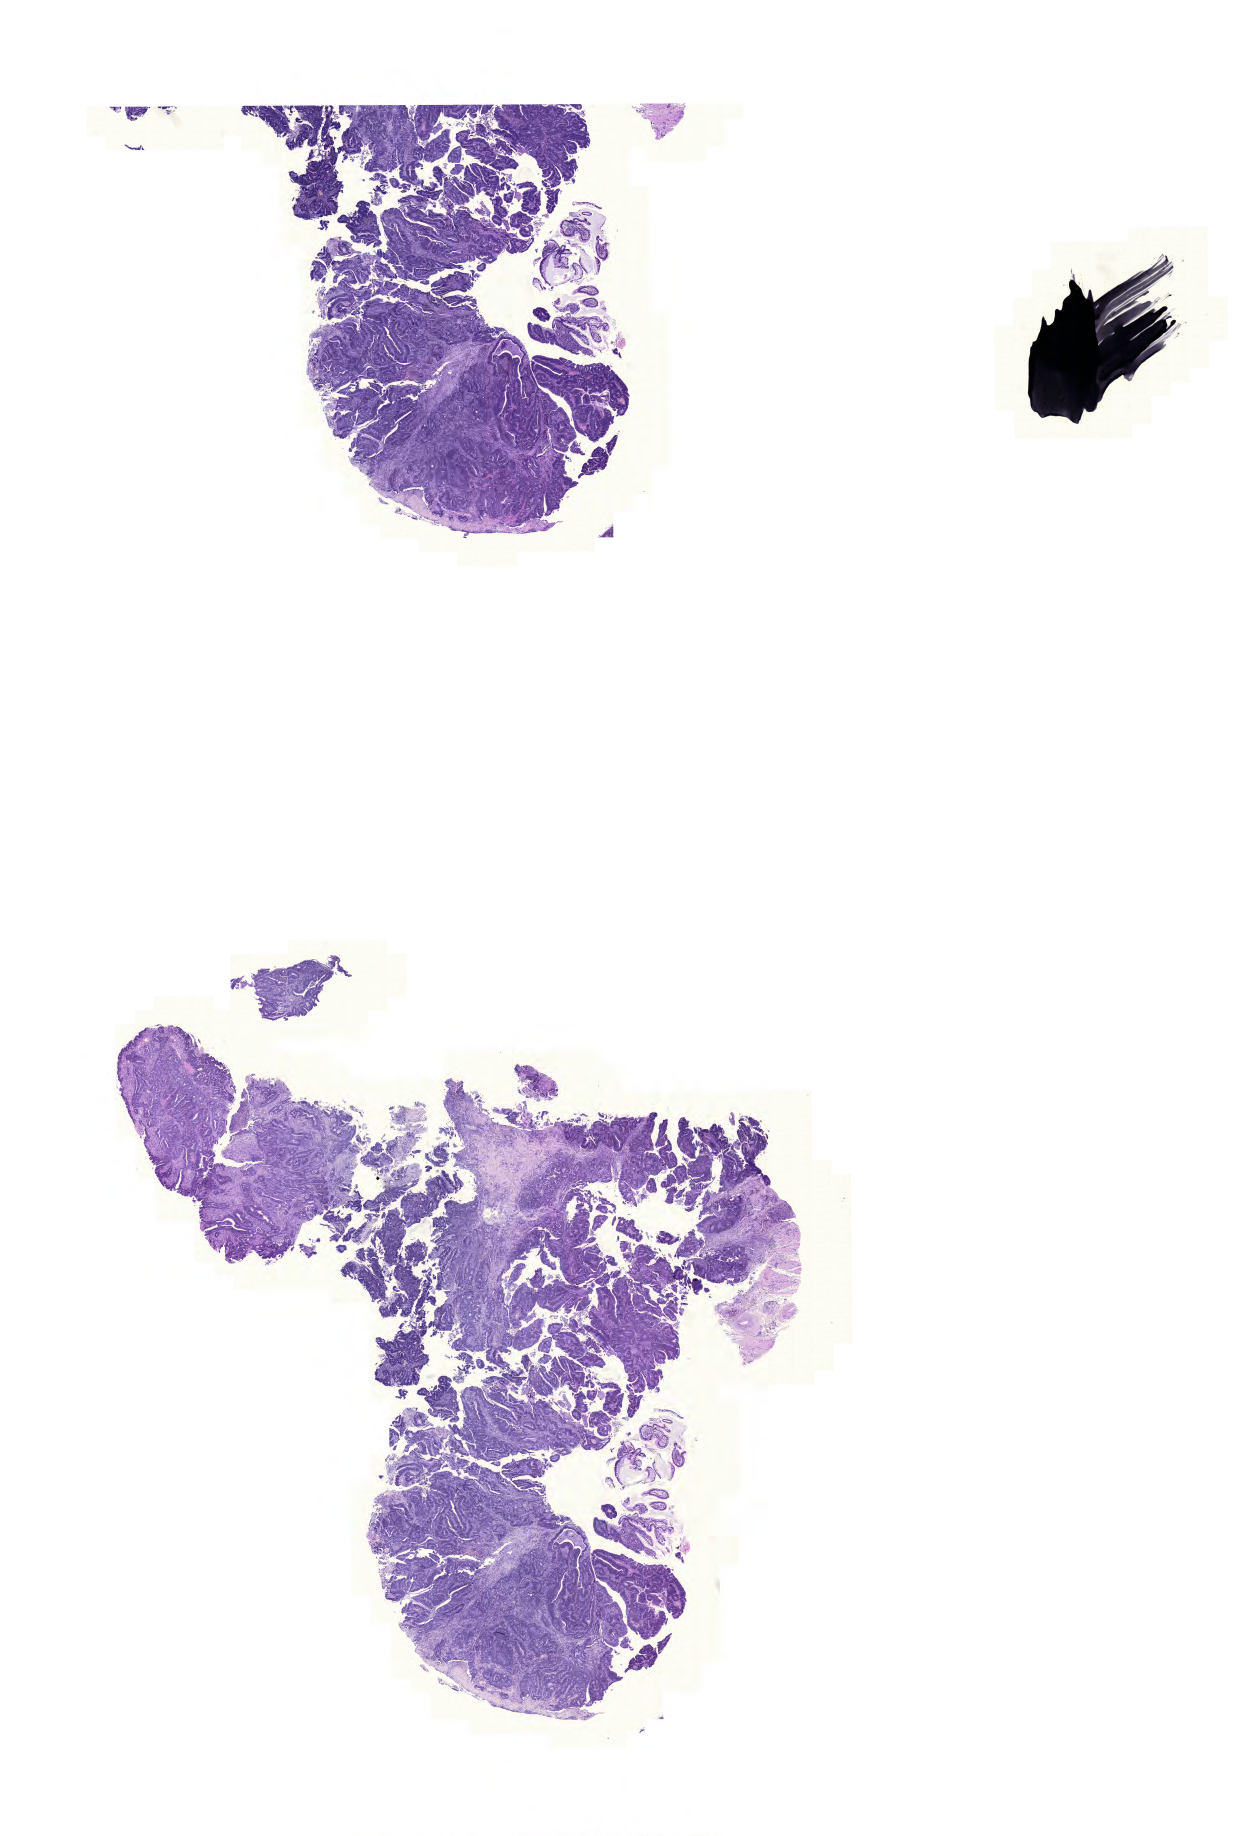
Digitized H&E-stained tissue section (whole slide) — a low-resolution overview of the entire scanned area, about 18.6 x 27.3 mm (from a 20x scan), formalin-fixed paraffin-embedded (FFPE) diagnostic section, sample: primary tumour, colon. Female patient; age at initial diagnosis 65 years.
• histologic diagnosis: Adenocarcinoma, NOS (cecum)
• TNM: T3 N0 M0
• AJCC pathologic stage: IIA
• lymph nodes positive (case pathology): 0 of 20 examined